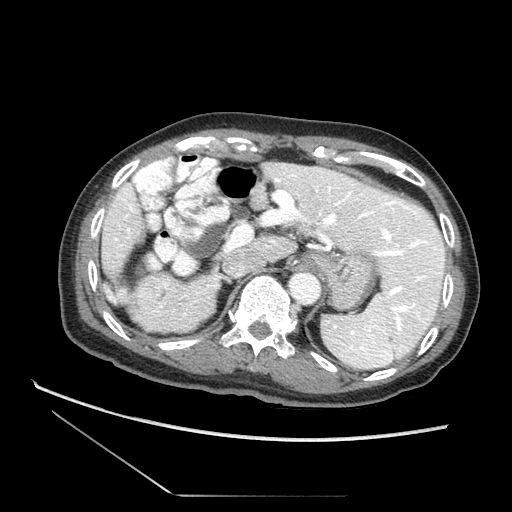
Contrast-enhanced abdominal CT (liver protocol), one axial slice; slice 53 of 73 in the series (ordered by position); soft-tissue window (W 400 / L 40 HU); 2.5 mm slice thickness; 512 × 512 image matrix. From the clinical record (not read from this slice): diagnosis: hepatocellular carcinoma (patient treated with transarterial chemoembolisation; whether this scan precedes or follows treatment is not stated here); TNM stage (as recorded): Stage-II; Child-Pugh class: A; tumour differentiation: moderately differentiated; tumour nodularity: multinodular.
Structures marked on this image (semi-automatic segmentation, software-assisted and operator-edited):
- liver parenchyma outside the tumour (the mass and vessels are separate outlines, so this box may not span the whole liver): bounding box [x1, y1, x2, y2] px = [102, 163, 452, 354]
- mass: [140, 280, 169, 307]
- liver vessels: [315, 186, 390, 239]